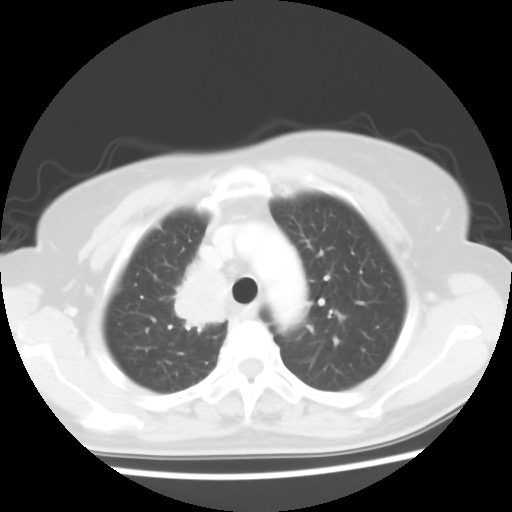
Chest CT, one axial slice. Position 44 of 56 along the scan axis. Reconstruction kernel STANDARD. 120 kVp. Lung window (W 1500 / L -600 HU). 512 × 512 image matrix, field of view 314 × 314 mm. Female patient, age 62 years. Case-level facts recorded for this patient, not image findings: clinical TNM (as recorded): T2 N1 M1a.
Outlined on this slice (rectangle marked by the reading radiologist):
- lung tumour (recorded histology: adenocarcinoma): bounding box (x1, y1, x2, y2) in pixels: (153, 245, 233, 348)